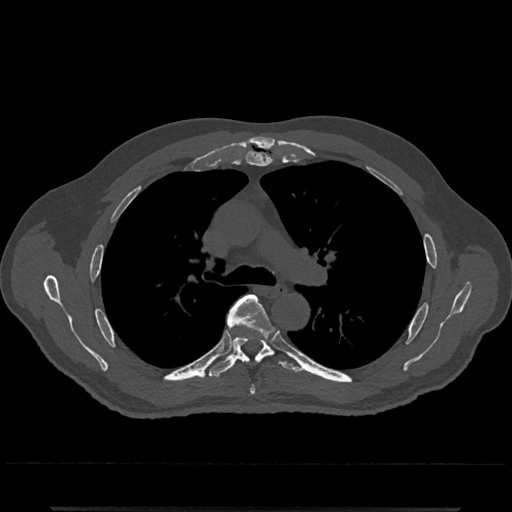
CT including the spine, one axial slice. Position 797 of 797 along the scan axis. Reconstruction kernel Br40s/3. 120 kVp. Bone window (W 1800 / L 400 HU). 512 × 512 image matrix, field of view 393 × 393 mm. Male patient, age 67 years. From the clinical record (not read from this slice): primary cancer: prostate.
Structures marked on this image (semi-automatic segmentation, software-assisted and operator-edited):
- T5 vertebra: box from (x=226, y=294) to (x=270, y=328) px
- T6 vertebra: (x=208, y=304)–(x=298, y=378)